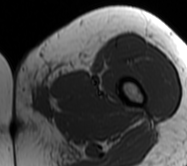
MRI of an extremity soft-tissue mass, one axial slice; position 11 of 62 along the scan axis; MR volume resampled by the dataset authors to the PET/CT grid (not the native acquisition matrix); 187 × 166 image matrix. Female patient. Case-level facts recorded for this patient, not image findings: histological type: leiomyosarcoma; grade: high; site of the primary tumour: groin.
Outlined on this slice (expert contour drawn on MRI and transferred to this co-registered scan by the dataset authors):
- gross tumour volume including surrounding oedema: box from (x=13, y=58) to (x=95, y=125) px